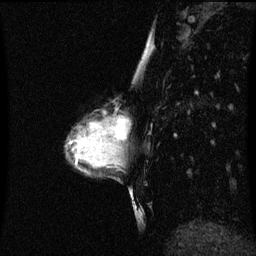
Breast MRI (dynamic contrast-enhanced), one sagittal slice; slice 29 of 60 in the series (ordered by position); dynamic contrast-enhanced series, image 2 of 3 at this slice position (ordered by acquisition); 1.5 T; TE 4.2 ms, TR 8.9 ms; 256 × 256 image matrix, field of view 200 × 200 mm. Patient: female, 33 years. Case-level facts recorded for this patient, not image findings: setting: breast cancer imaged before/during neoadjuvant chemotherapy; receptor status: HER2-positive.
Outlined on this slice (semi-automatic segmentation, software-assisted and operator-edited):
- analysis volume of interest (the breast-tissue region the enhancement analysis was run in; not a lesion): box from (x=107, y=110) to (x=124, y=147) px
- tumour enhancement mask (voxels above the 70 % enhancement threshold inside the analysis volume of interest): (x=115, y=116)–(x=123, y=141)